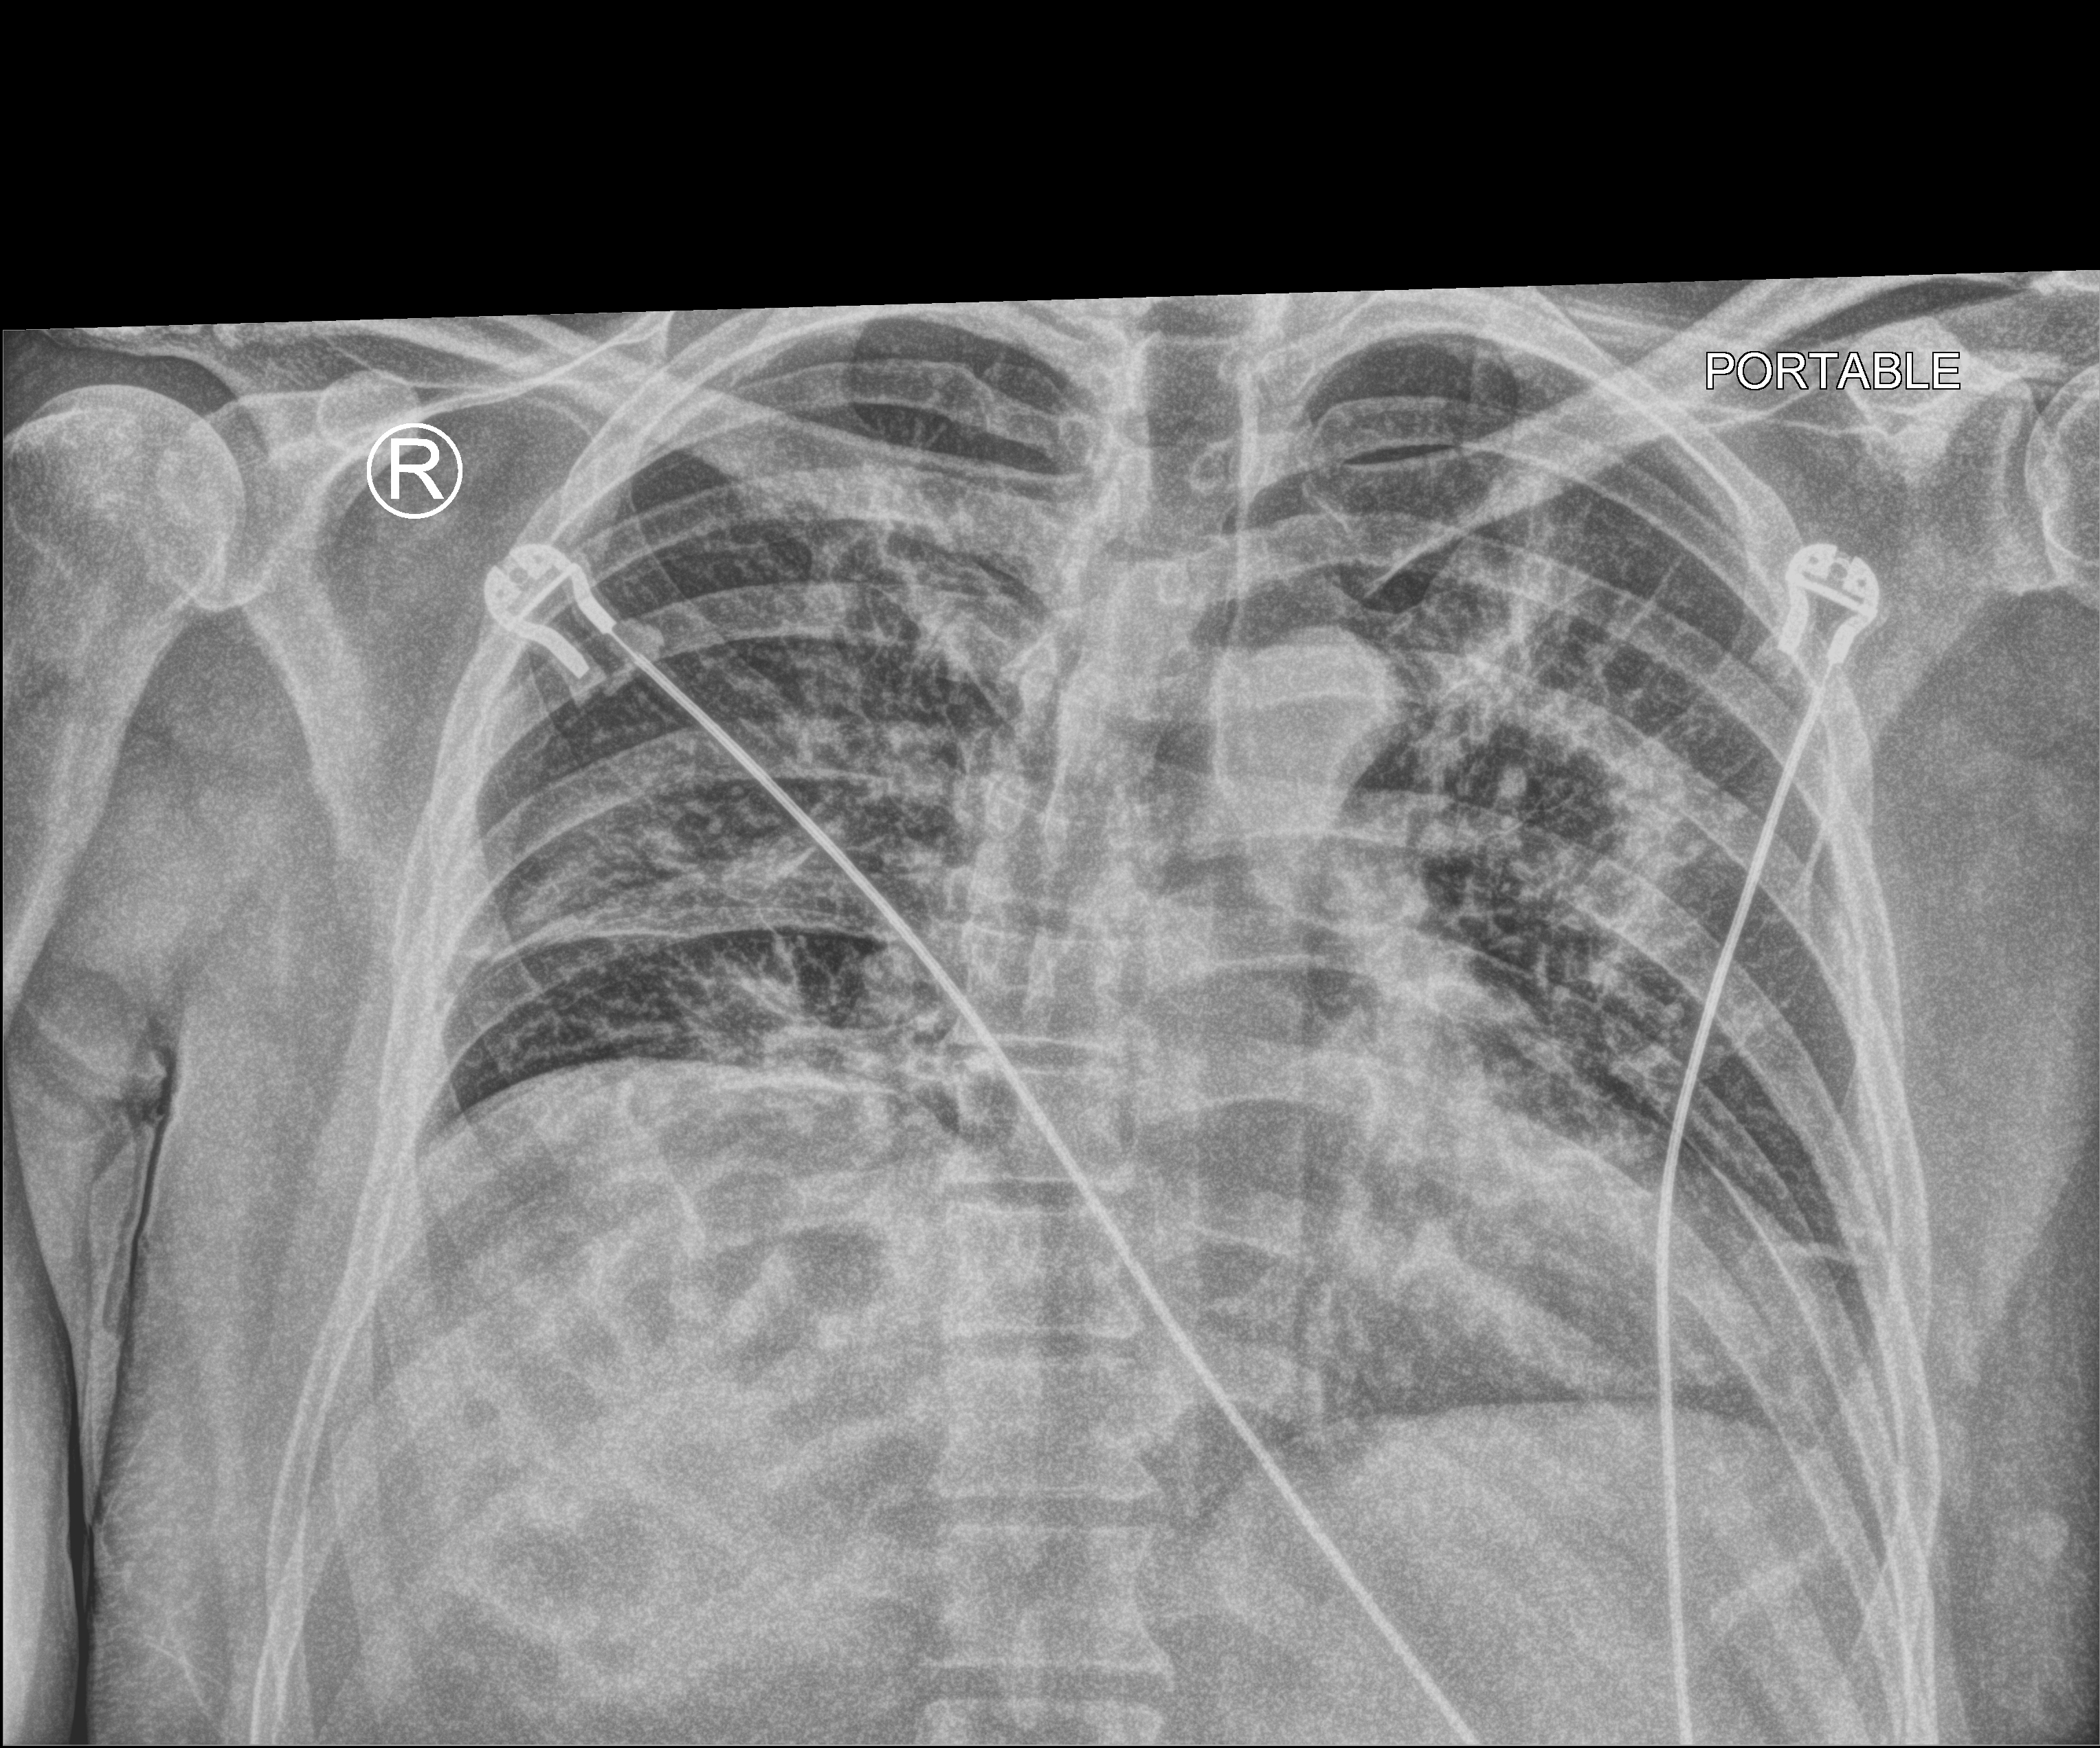
Bedside chest radiograph (computed radiography); anteroposterior (AP) projection. Patient hospitalised with COVID-19; male, aged 18–59 years.
From the hospital-stay record, not from the radiograph (when in the stay this image was taken is not recorded):
- admitted to intensive care during this hospital stay: no
- mechanically ventilated during this hospital stay: no